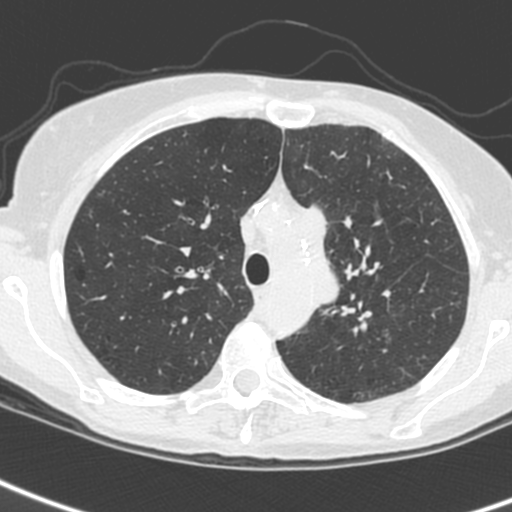
Low-dose screening chest CT, one axial slice. Slice 185 of 242 in the series (ordered by position). 120 kVp. Lung window (W 1500 / L -600 HU). 1.3 mm slice thickness. 512 × 512 image matrix.
Structures marked on this image (outlined manually by an expert reader):
- lesion 3 (tumor, upper lobe of left lung): box from (x=302, y=205) to (x=340, y=305) px